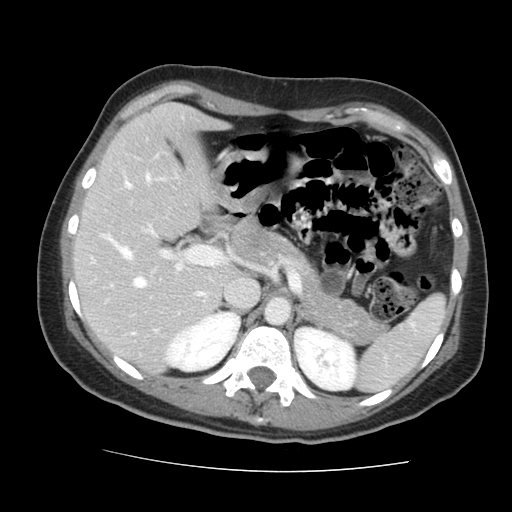
Contrast-enhanced abdominal CT, one axial slice; position 93 of 144 along the scan axis; intravenous contrast given; soft-tissue window (W 400 / L 40 HU); 2.5 mm slice thickness; 512 × 512 image matrix, field of view 333 × 333 mm. Female patient, age 46 years. Case-level facts recorded for this patient, not image findings: diagnosis: colorectal cancer liver metastases, imaged before liver resection; multiple liver metastases: no; largest metastasis: 2.8 cm; chemotherapy before resection: yes.
Annotated regions visible in this slice (outlined manually by an expert reader):
- hepatic veins: bounding box <124,174,203,296> (left, top, right, bottom; pixels)
- liver: <77,106,225,370>
- planned liver remnant (the part of the liver to remain after resection): <77,106,225,370>
- portal vein (with intrahepatic branches): <103,225,225,332>